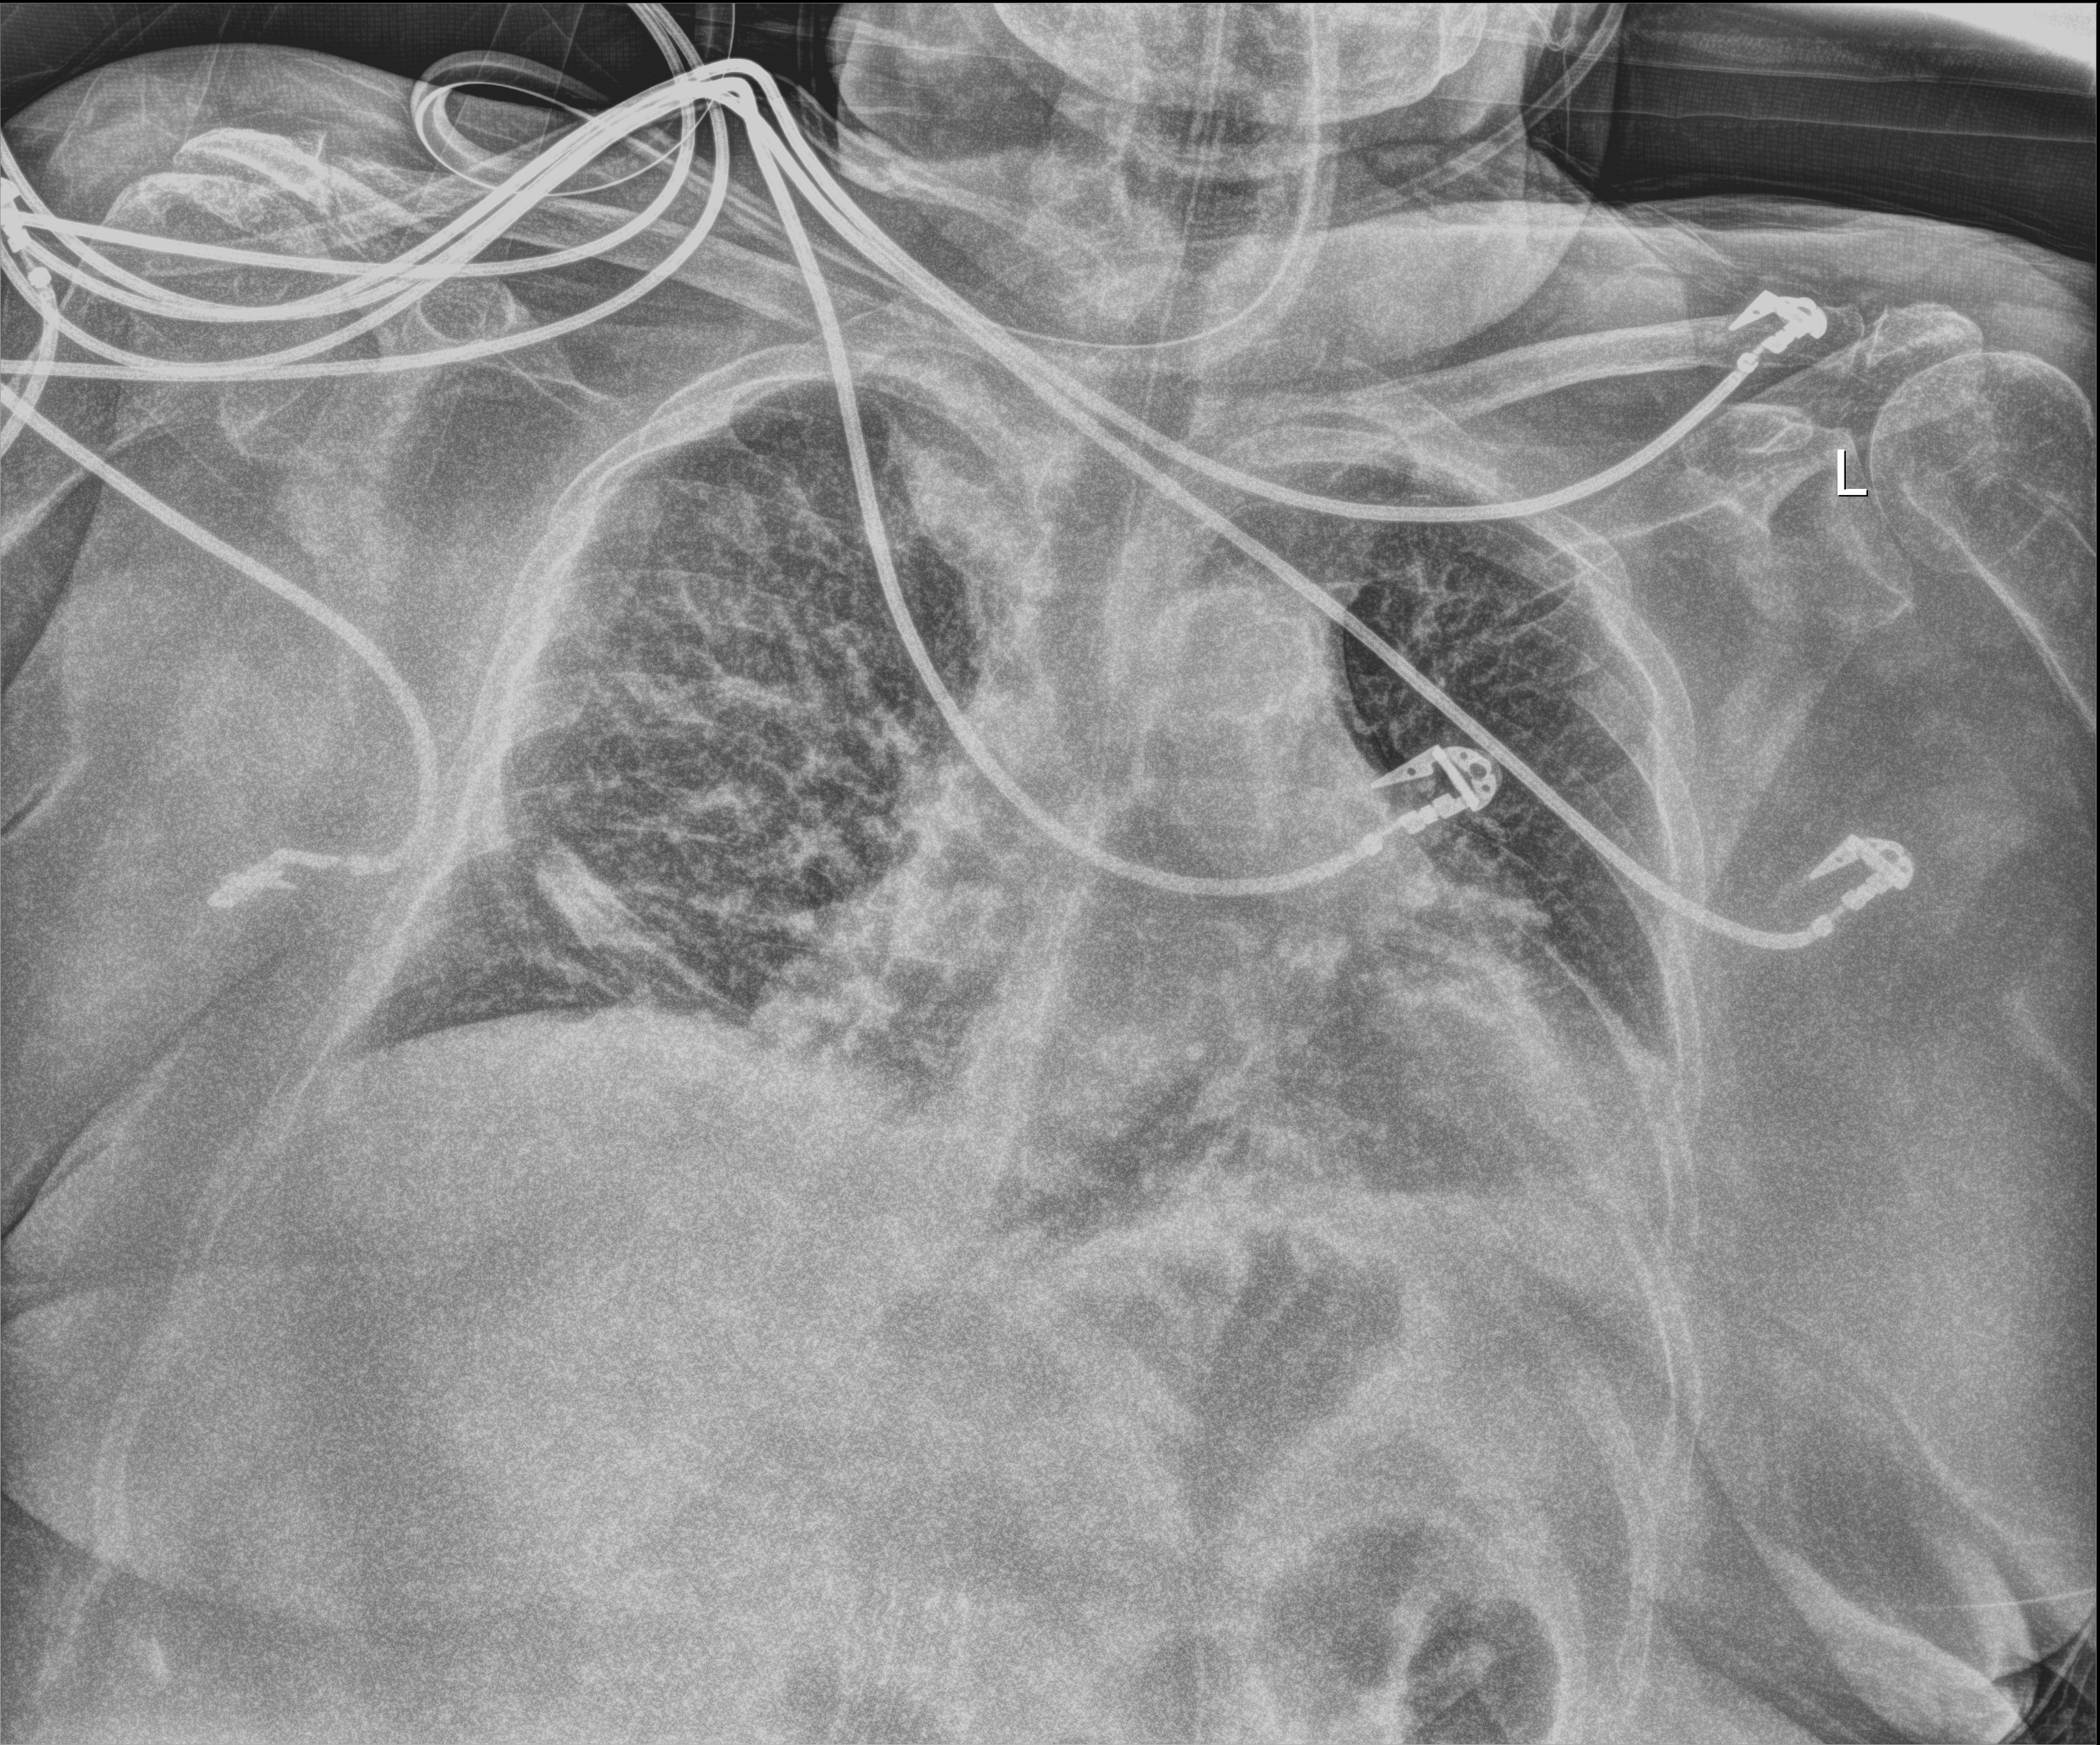
Chest radiograph (digital radiography). Female patient hospitalised with COVID-19, age 60–74 years.
Admission-level facts for this patient (not findings on this image; timing relative to this image not recorded): admitted to intensive care during this hospital stay: yes; mechanically ventilated during this hospital stay: no; length of hospital stay: 9 days.